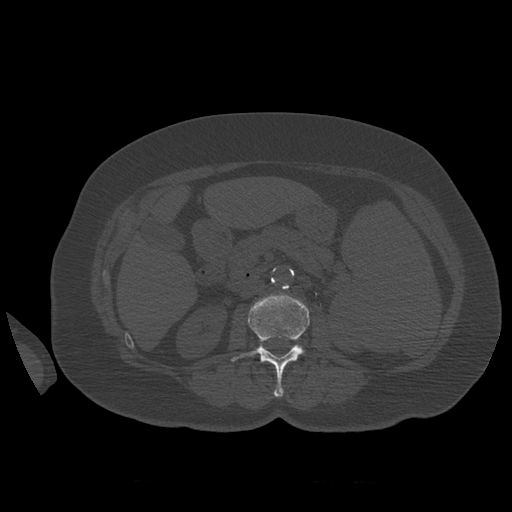
CT including the spine, one axial slice. Slice 252 of 399 in the series (ordered by position). 120 kVp. Bone window (W 1800 / L 400 HU). 1.25 mm slice thickness. 512 × 512 image matrix, field of view 404 × 404 mm. Patient age 81 years. Case-level facts recorded for this patient, not image findings: primary cancer: renal; vertebrae with lytic lesions (as recorded): L1.
Annotated regions visible in this slice (semi-automatic segmentation, software-assisted and operator-edited):
- L2 vertebra: bounding box <231,294,310,397> (left, top, right, bottom; pixels)